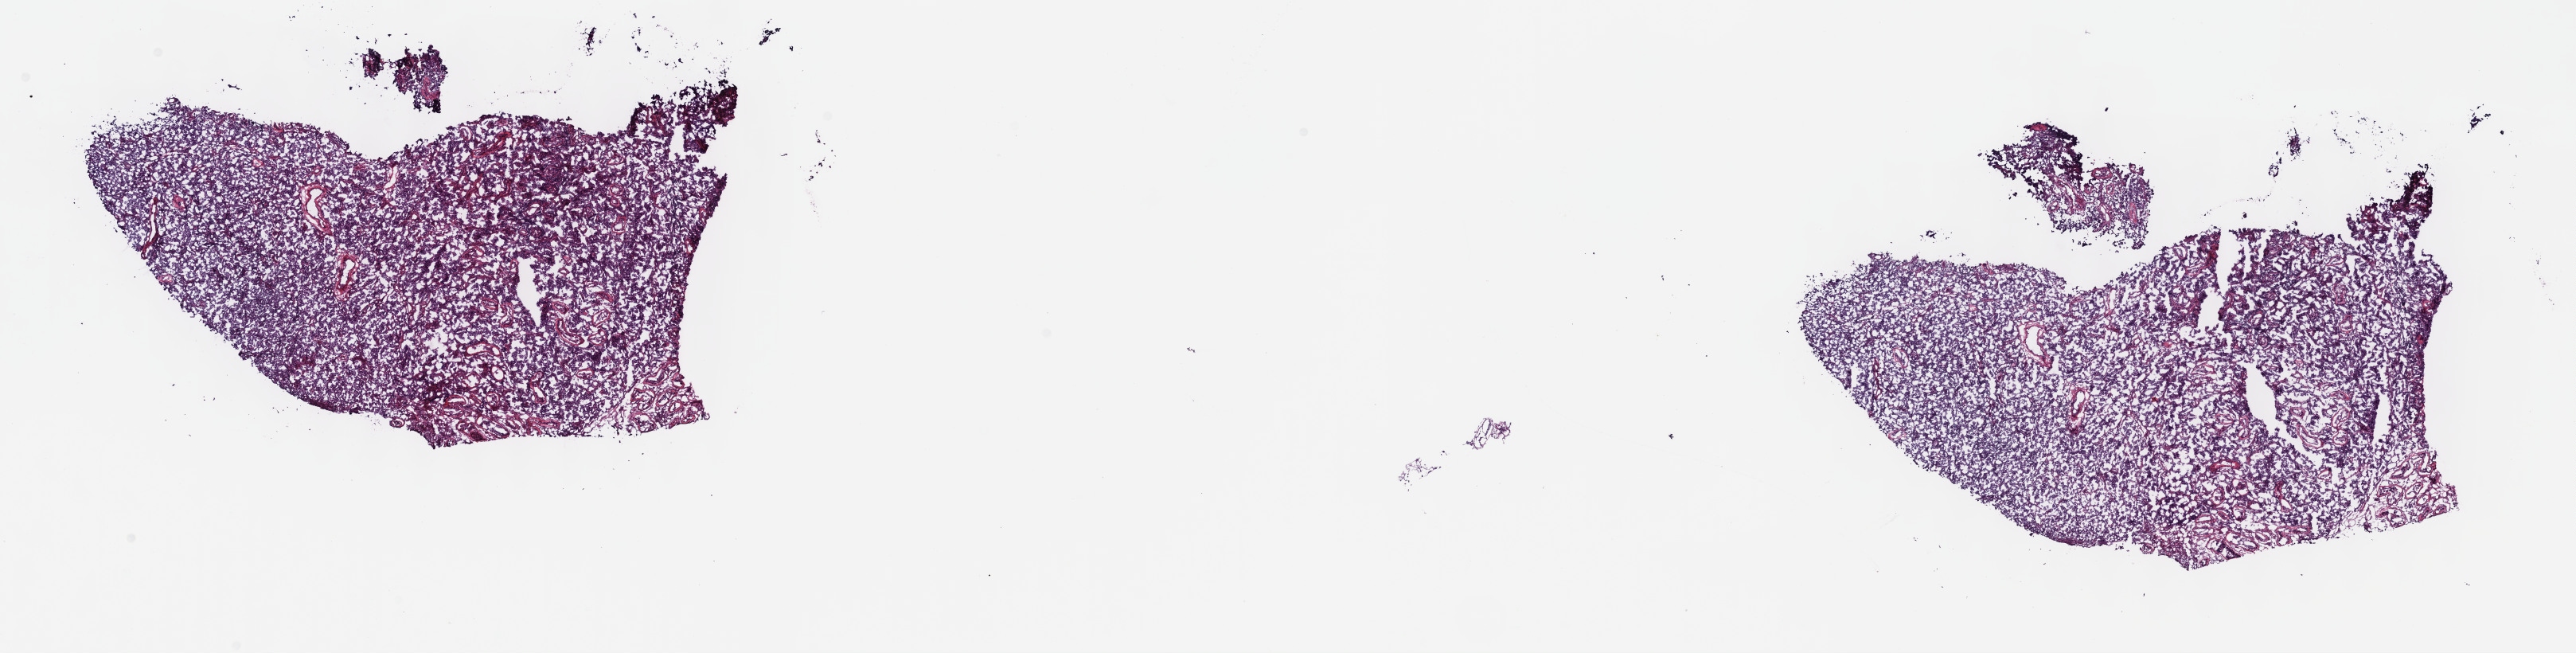
H&E whole-slide image — whole scanned area (about 26.2 x 6.6 mm, acquisition: 40x scan) shown as a low-resolution overview; frozen section; sample: primary tumour, testis. Male, age 29 years at initial diagnosis. Slide review estimates, as recorded: tumour cells 100%, tumour nuclei 80%, normal cells 0%, stromal cells 0%, necrosis 0%. Inflammatory infiltration, as recorded: lymphocyte infiltration 0%, monocyte infiltration 0%, neutrophil infiltration 0%.
AJCC pathologic stage: IA (7th edition). Pathologic diagnosis: Seminoma, NOS. TNM: T1 NX M0.